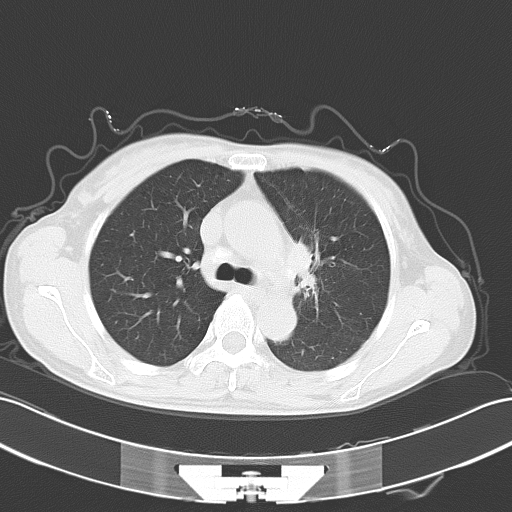
Chest CT, one axial slice. Position 38 of 54 along the scan axis. Reconstruction kernel B70f. Lung window (W 1500 / L -600 HU). 512 × 512 image matrix. Patient: female, 50 years. Case-level facts recorded for this patient, not image findings: clinical TNM (as recorded): T2a N1 M1c.
Outlined on this slice (rectangle marked by the reading radiologist):
- lung tumour (recorded histology: adenocarcinoma): bounding box (x1, y1, x2, y2) in pixels: (292, 233, 318, 280)